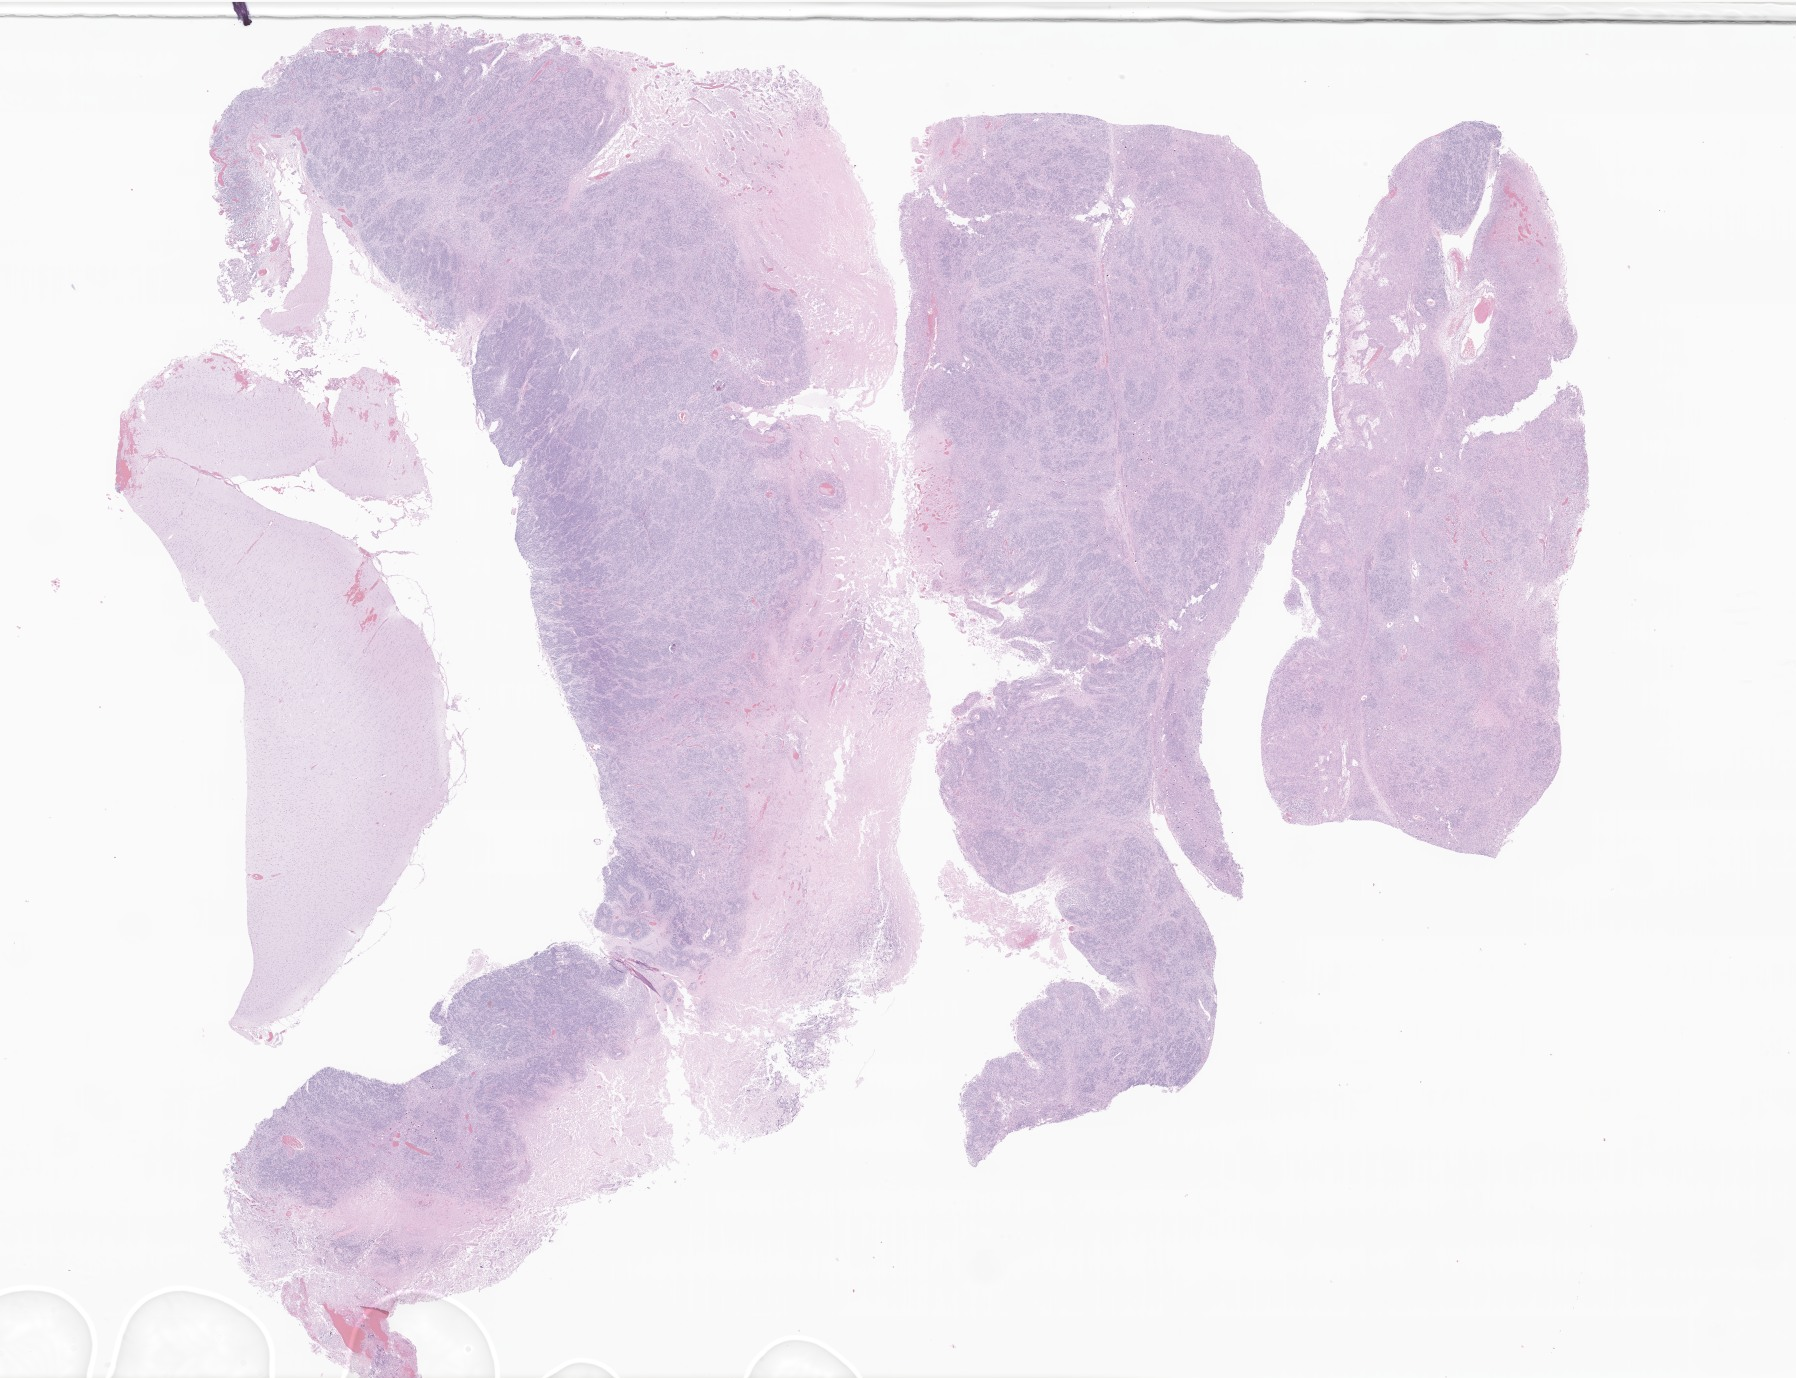
Haematoxylin and eosin whole-slide image of tumor tissue from the brain — shown as a low-resolution overview of the whole scanned area (about 30.3 x 23.2 mm). FFPE section. Patient: male, age 399 days (about 1.1 years).
Diagnosis (ICD-O-3 morphology term): Neoplasm, uncertain whether benign or malignant.